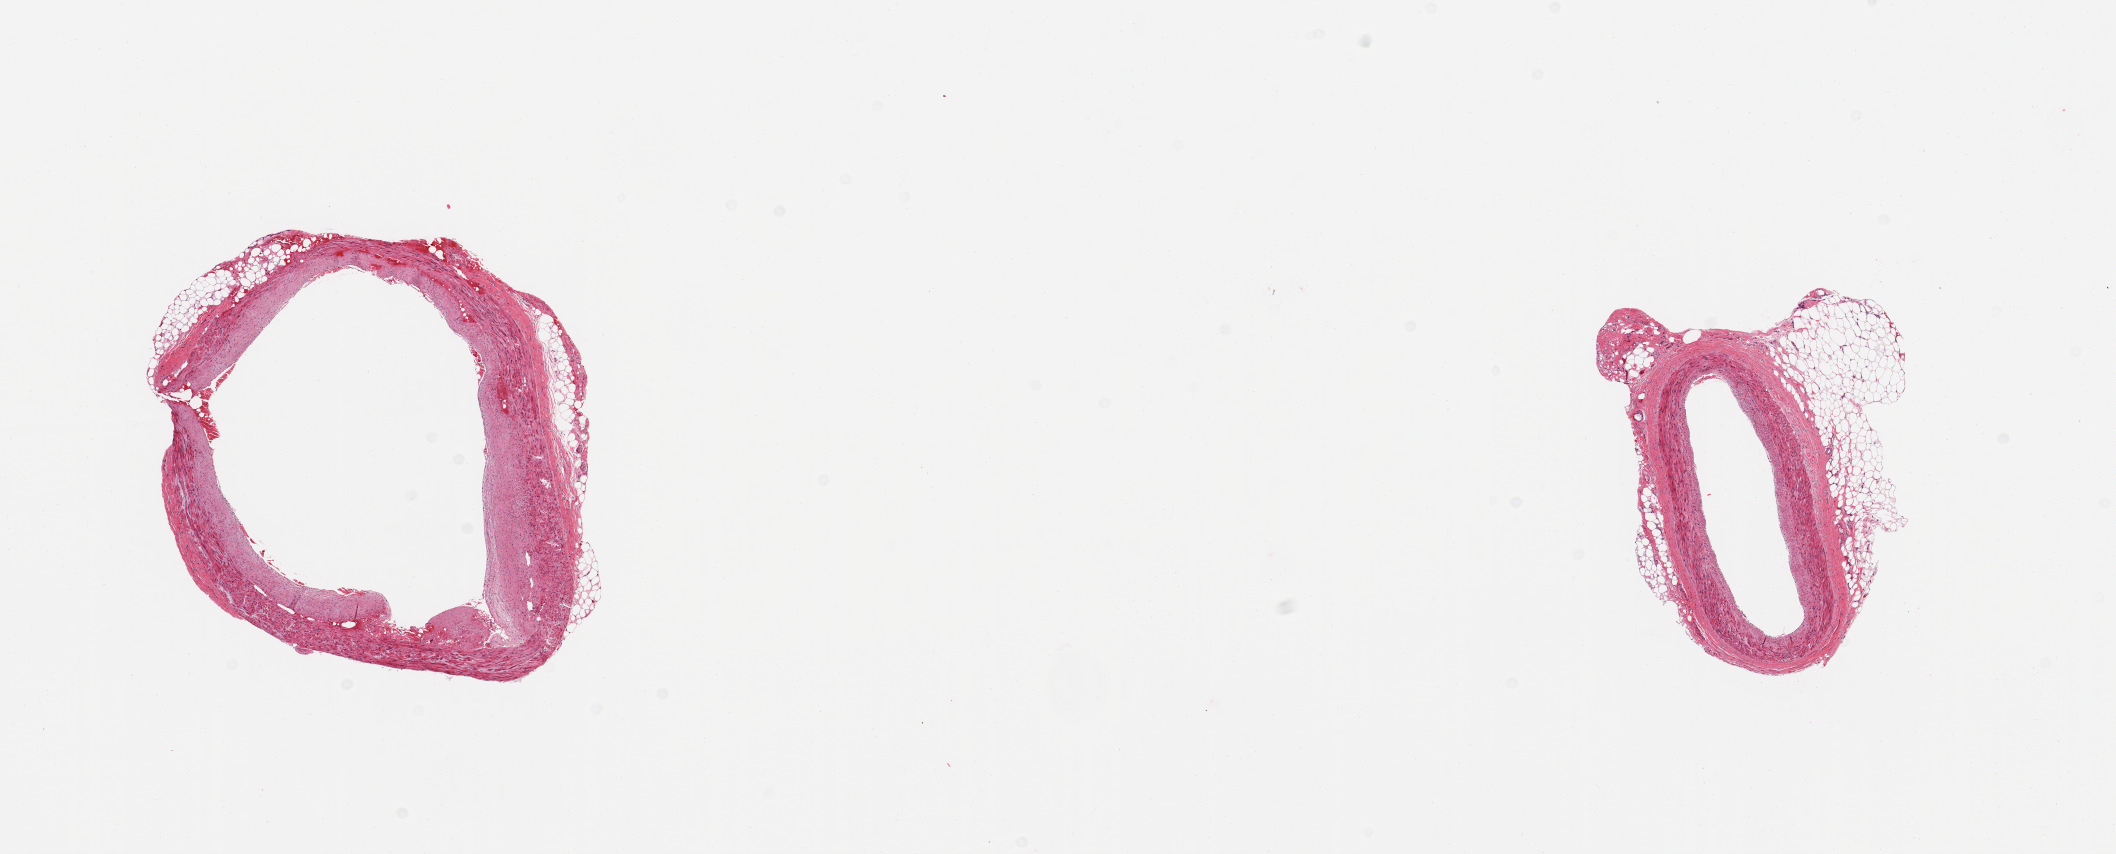
Haematoxylin and eosin whole-slide image — whole scanned area (about 16.7 x 6.8 mm) shown as a low-resolution overview, PAXgene-fixed, paraffin-embedded tissue, sampled site (target tissue): coronary artery, tissue donor sample. Donor: female.
Pathologist's review note for this sample: 2 pieces; non-occlusive sclerotic plaque on 1; 30% & 10% external fat.